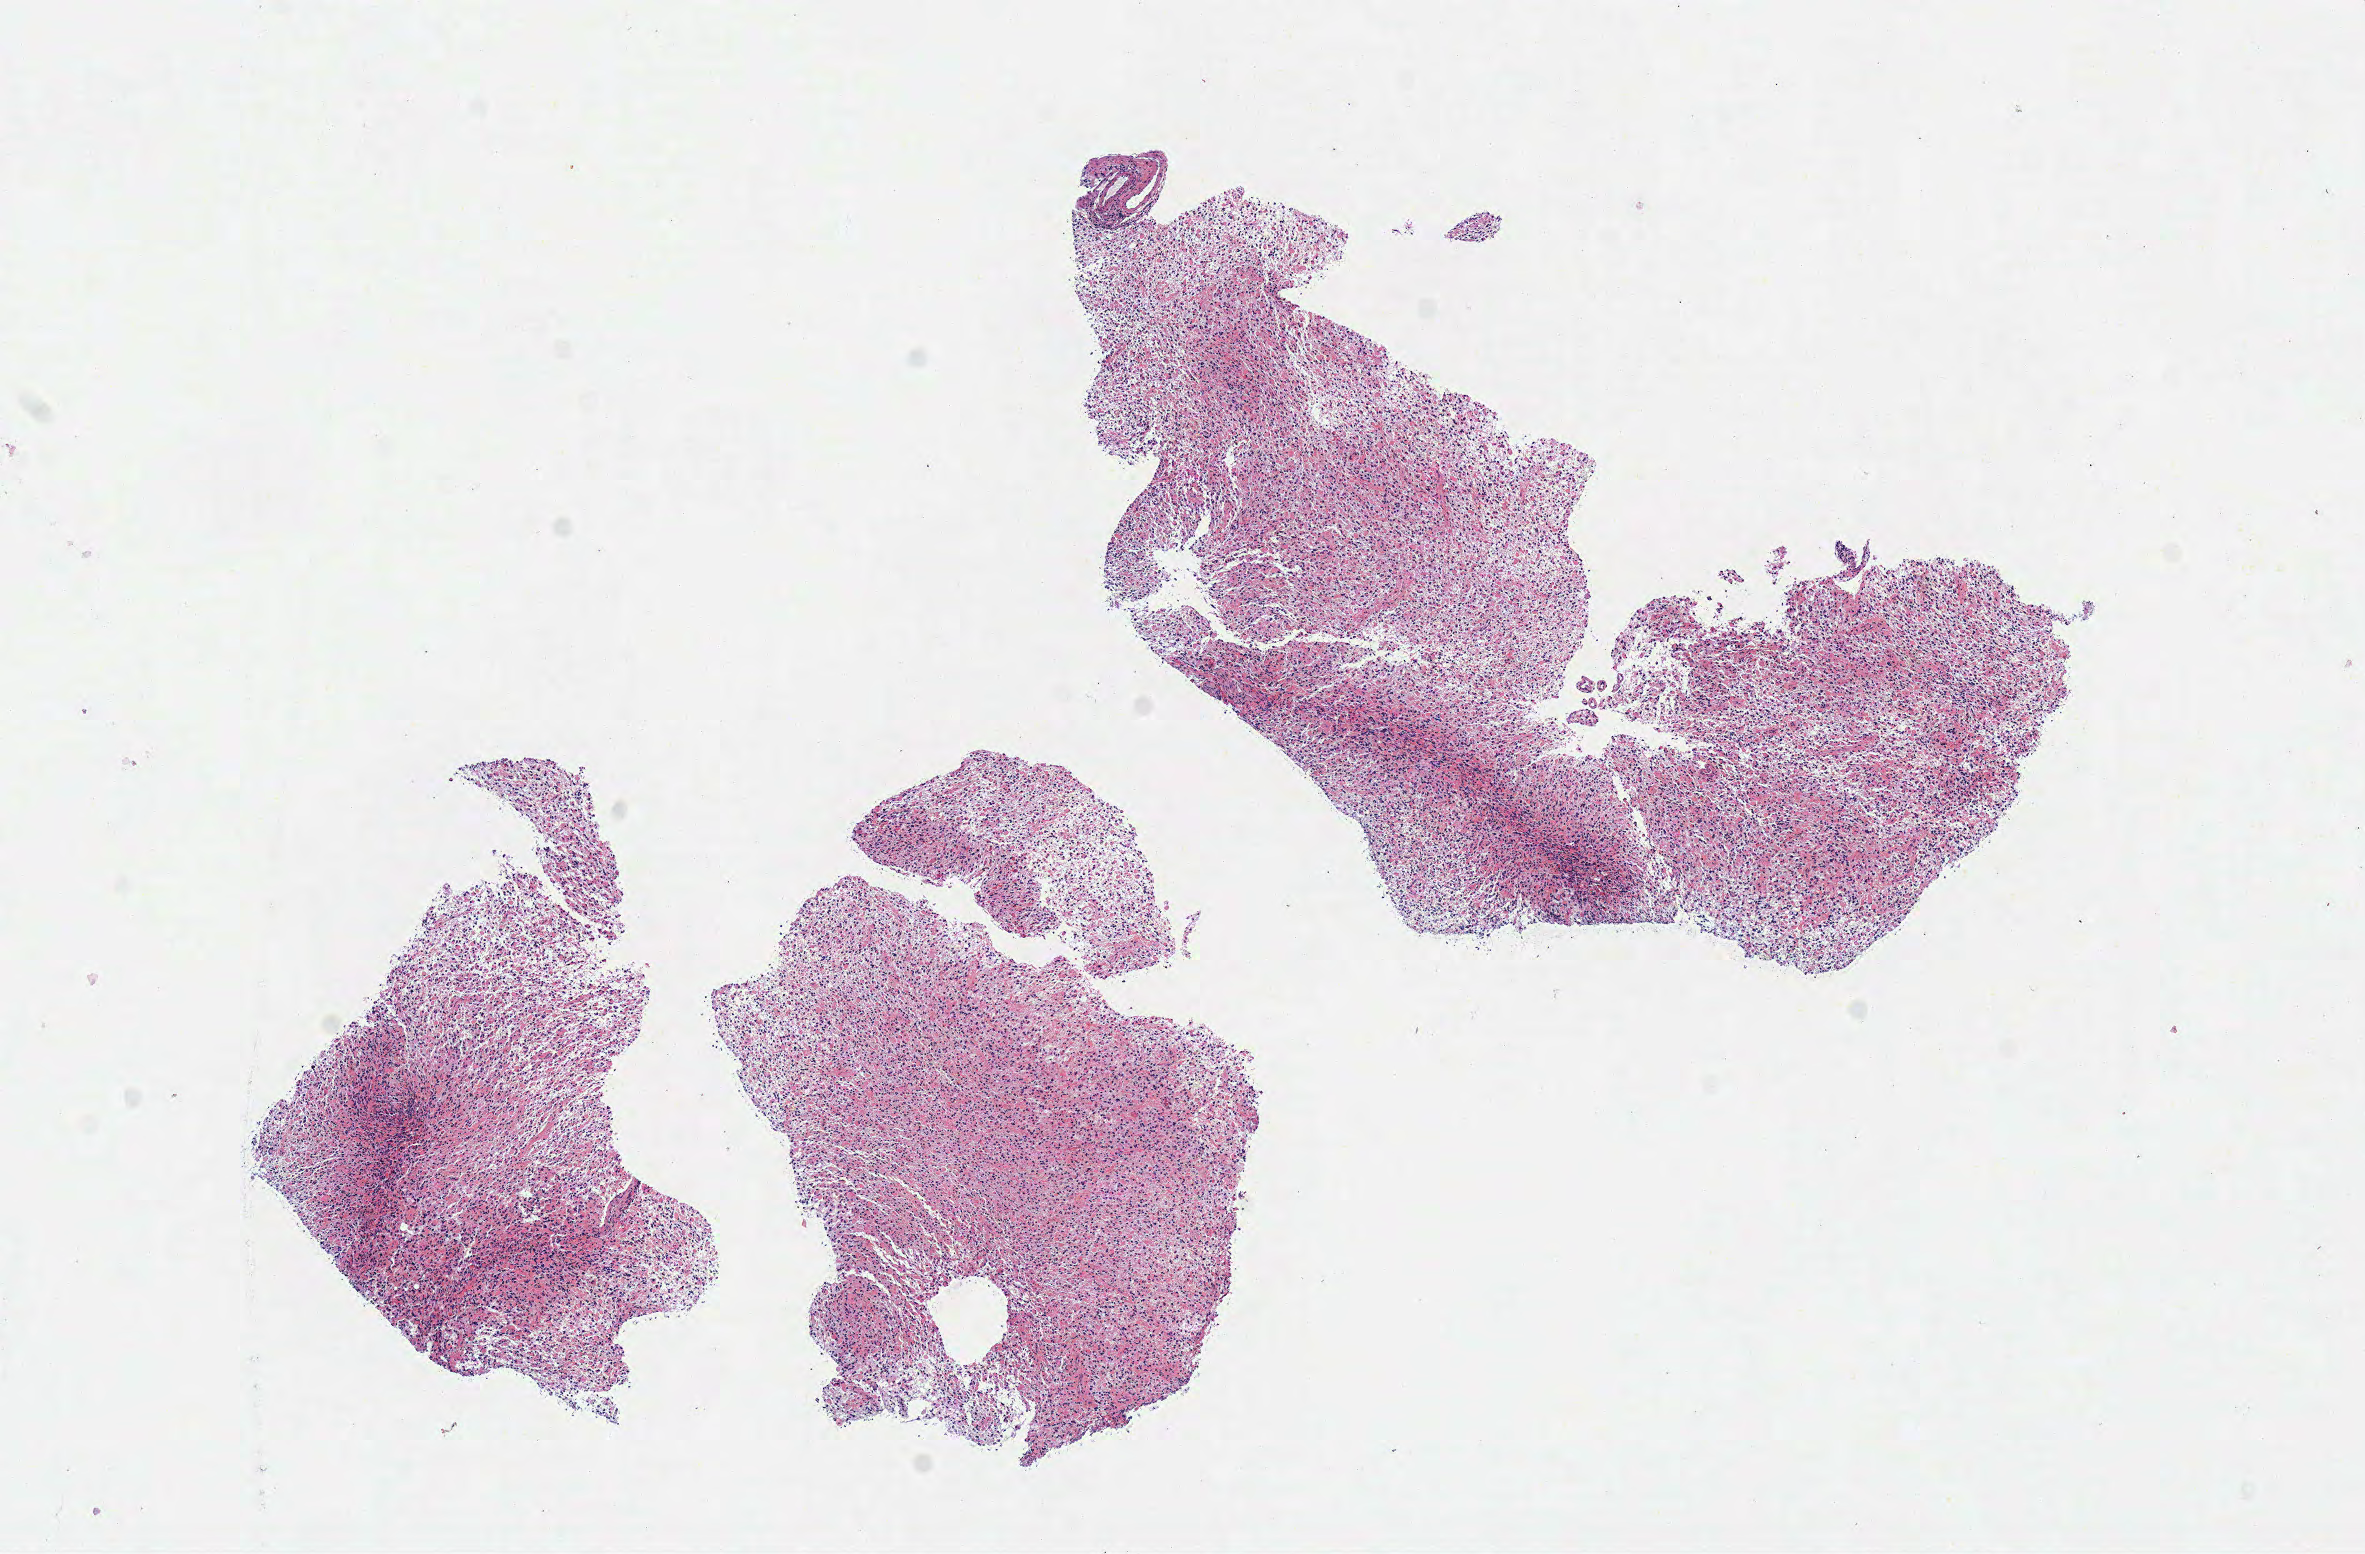
Digitized Hematoxylin and eosin (H&E) stained tissue section (whole slide), shown as a low-resolution overview of the whole scanned area (about 9.3 x 6.1 mm, from a 40x scan), frozen section from the top of the tissue portion, sample: primary tumour, brain. Female patient; age at initial diagnosis 31 years. Histologic grade: G3 (poorly differentiated). Pathologist review of this section (percent, as recorded): tumour cells 100%, tumour nuclei 80%, normal cells 0%, stromal cells 0%, necrosis 0%.
Laterality: right. Histologic diagnosis: Mixed glioma (cerebrum).